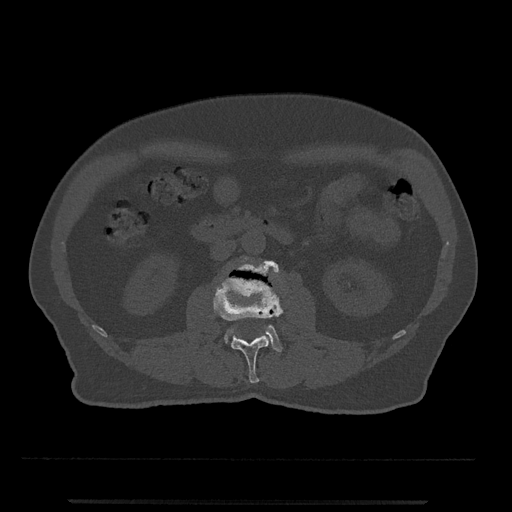
CT including the spine, one axial slice. Slice 244 of 797 in the series (ordered by position). Reconstruction kernel Br40s/3. 120 kVp. Bone window (W 1800 / L 400 HU). 0.5 mm slice thickness. 512 × 512 image matrix, field of view 419 × 419 mm. Male patient, age 63 years. From the clinical record (not read from this slice): primary cancer: prostate.
Outlined on this slice (semi-automatic segmentation, software-assisted and operator-edited):
- L2 vertebra: bounding box (x1, y1, x2, y2) in pixels: (213, 265, 283, 383)
- L3 vertebra: (225, 261, 283, 352)